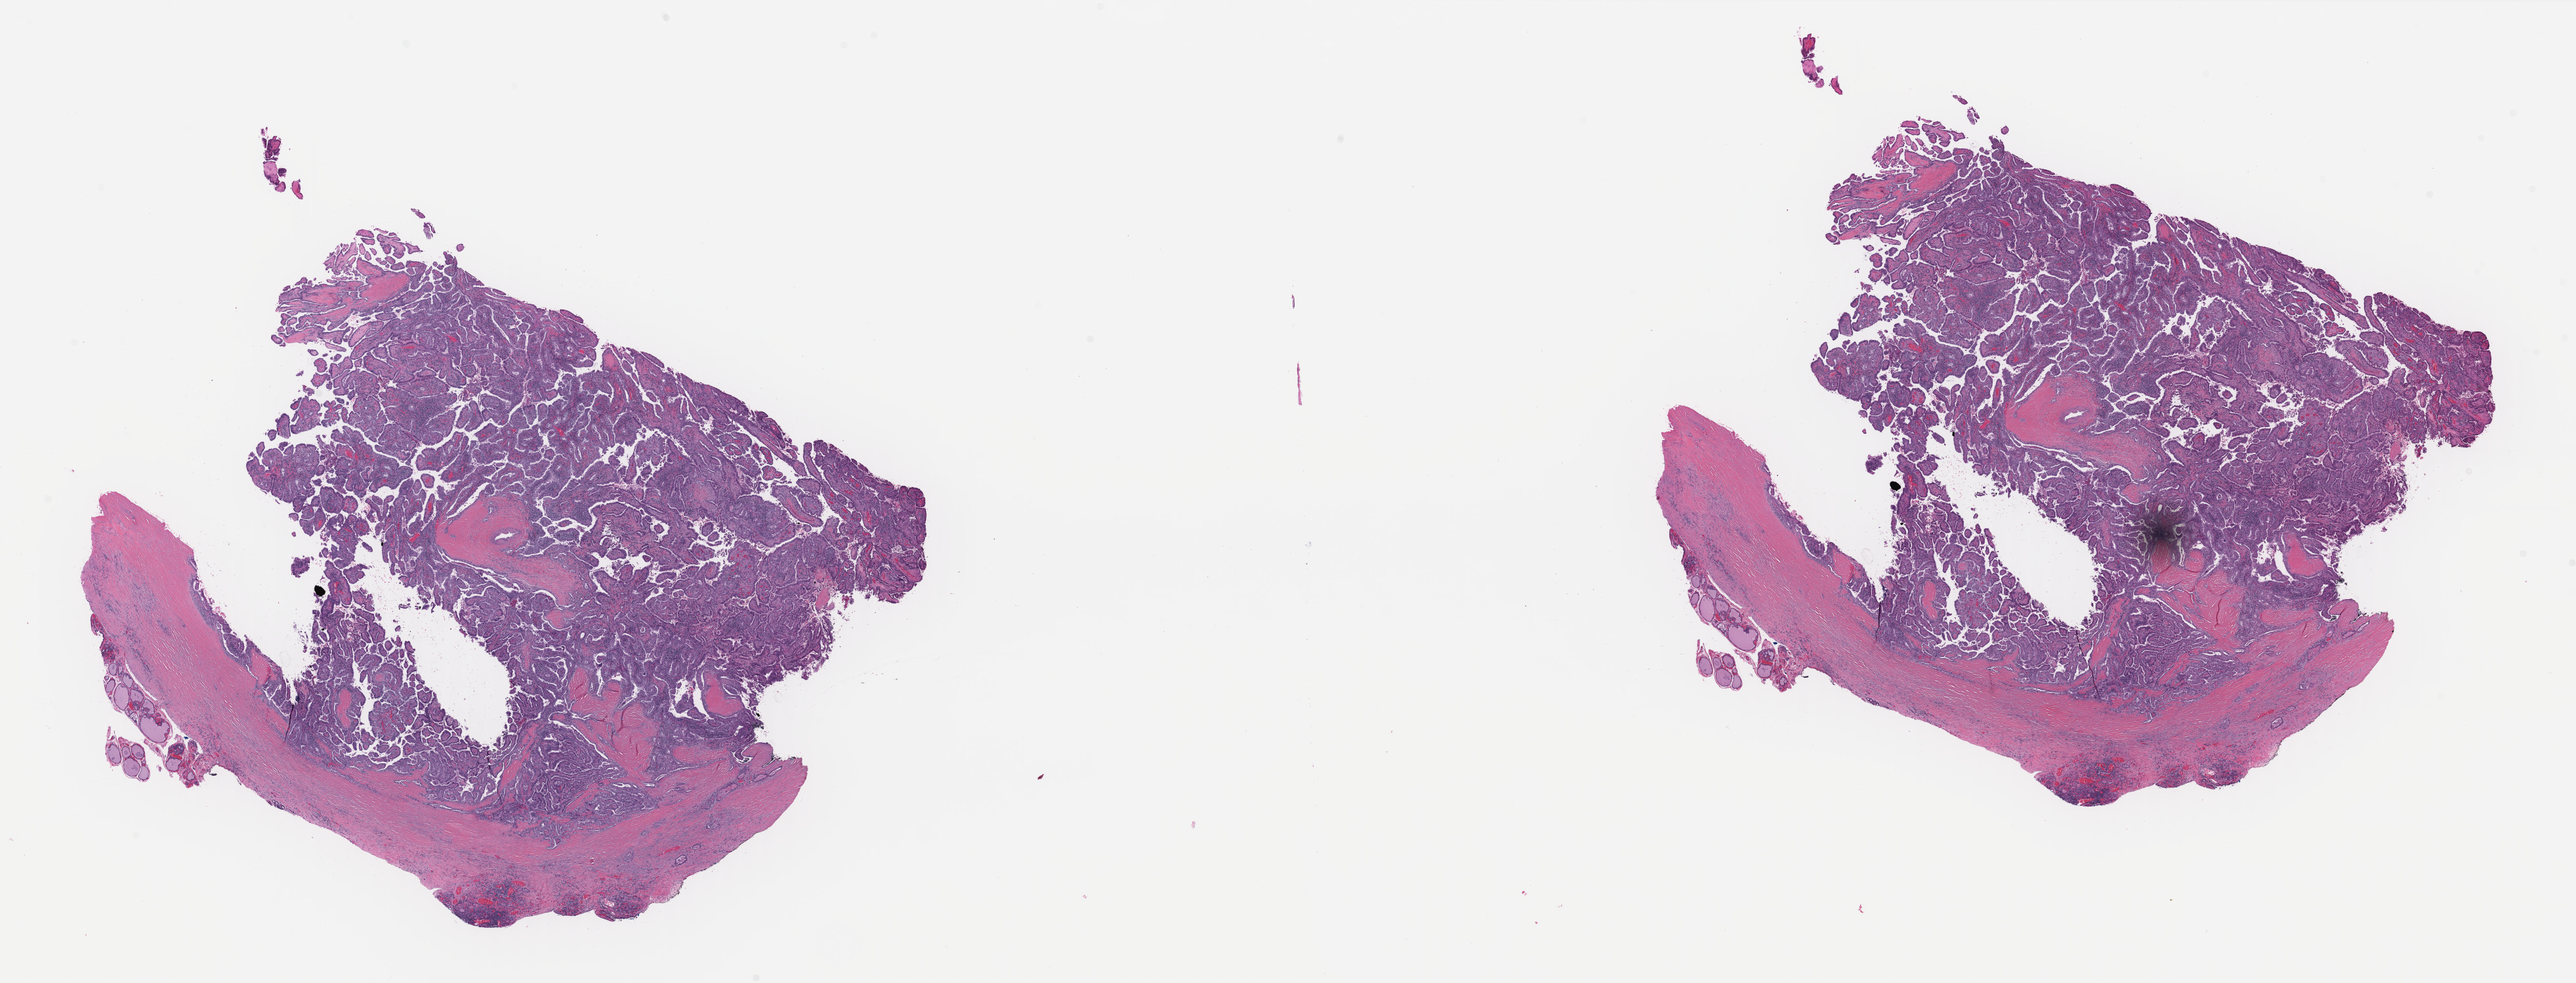
Digitized Hematoxylin and eosin (H&E) stained tissue section (whole slide), shown as a low-resolution overview of the whole scanned area (about 31.1 x 11.9 mm, acquisition: 40x scan). Formalin-fixed paraffin-embedded (FFPE) diagnostic section. Sample: primary tumour, thyroid. Female, age 36 years at initial diagnosis.
* AJCC pathologic stage: I
* diagnosis: Papillary adenocarcinoma, NOS (thyroid gland)
* lymph nodes positive (case pathology): 0 of 8 examined